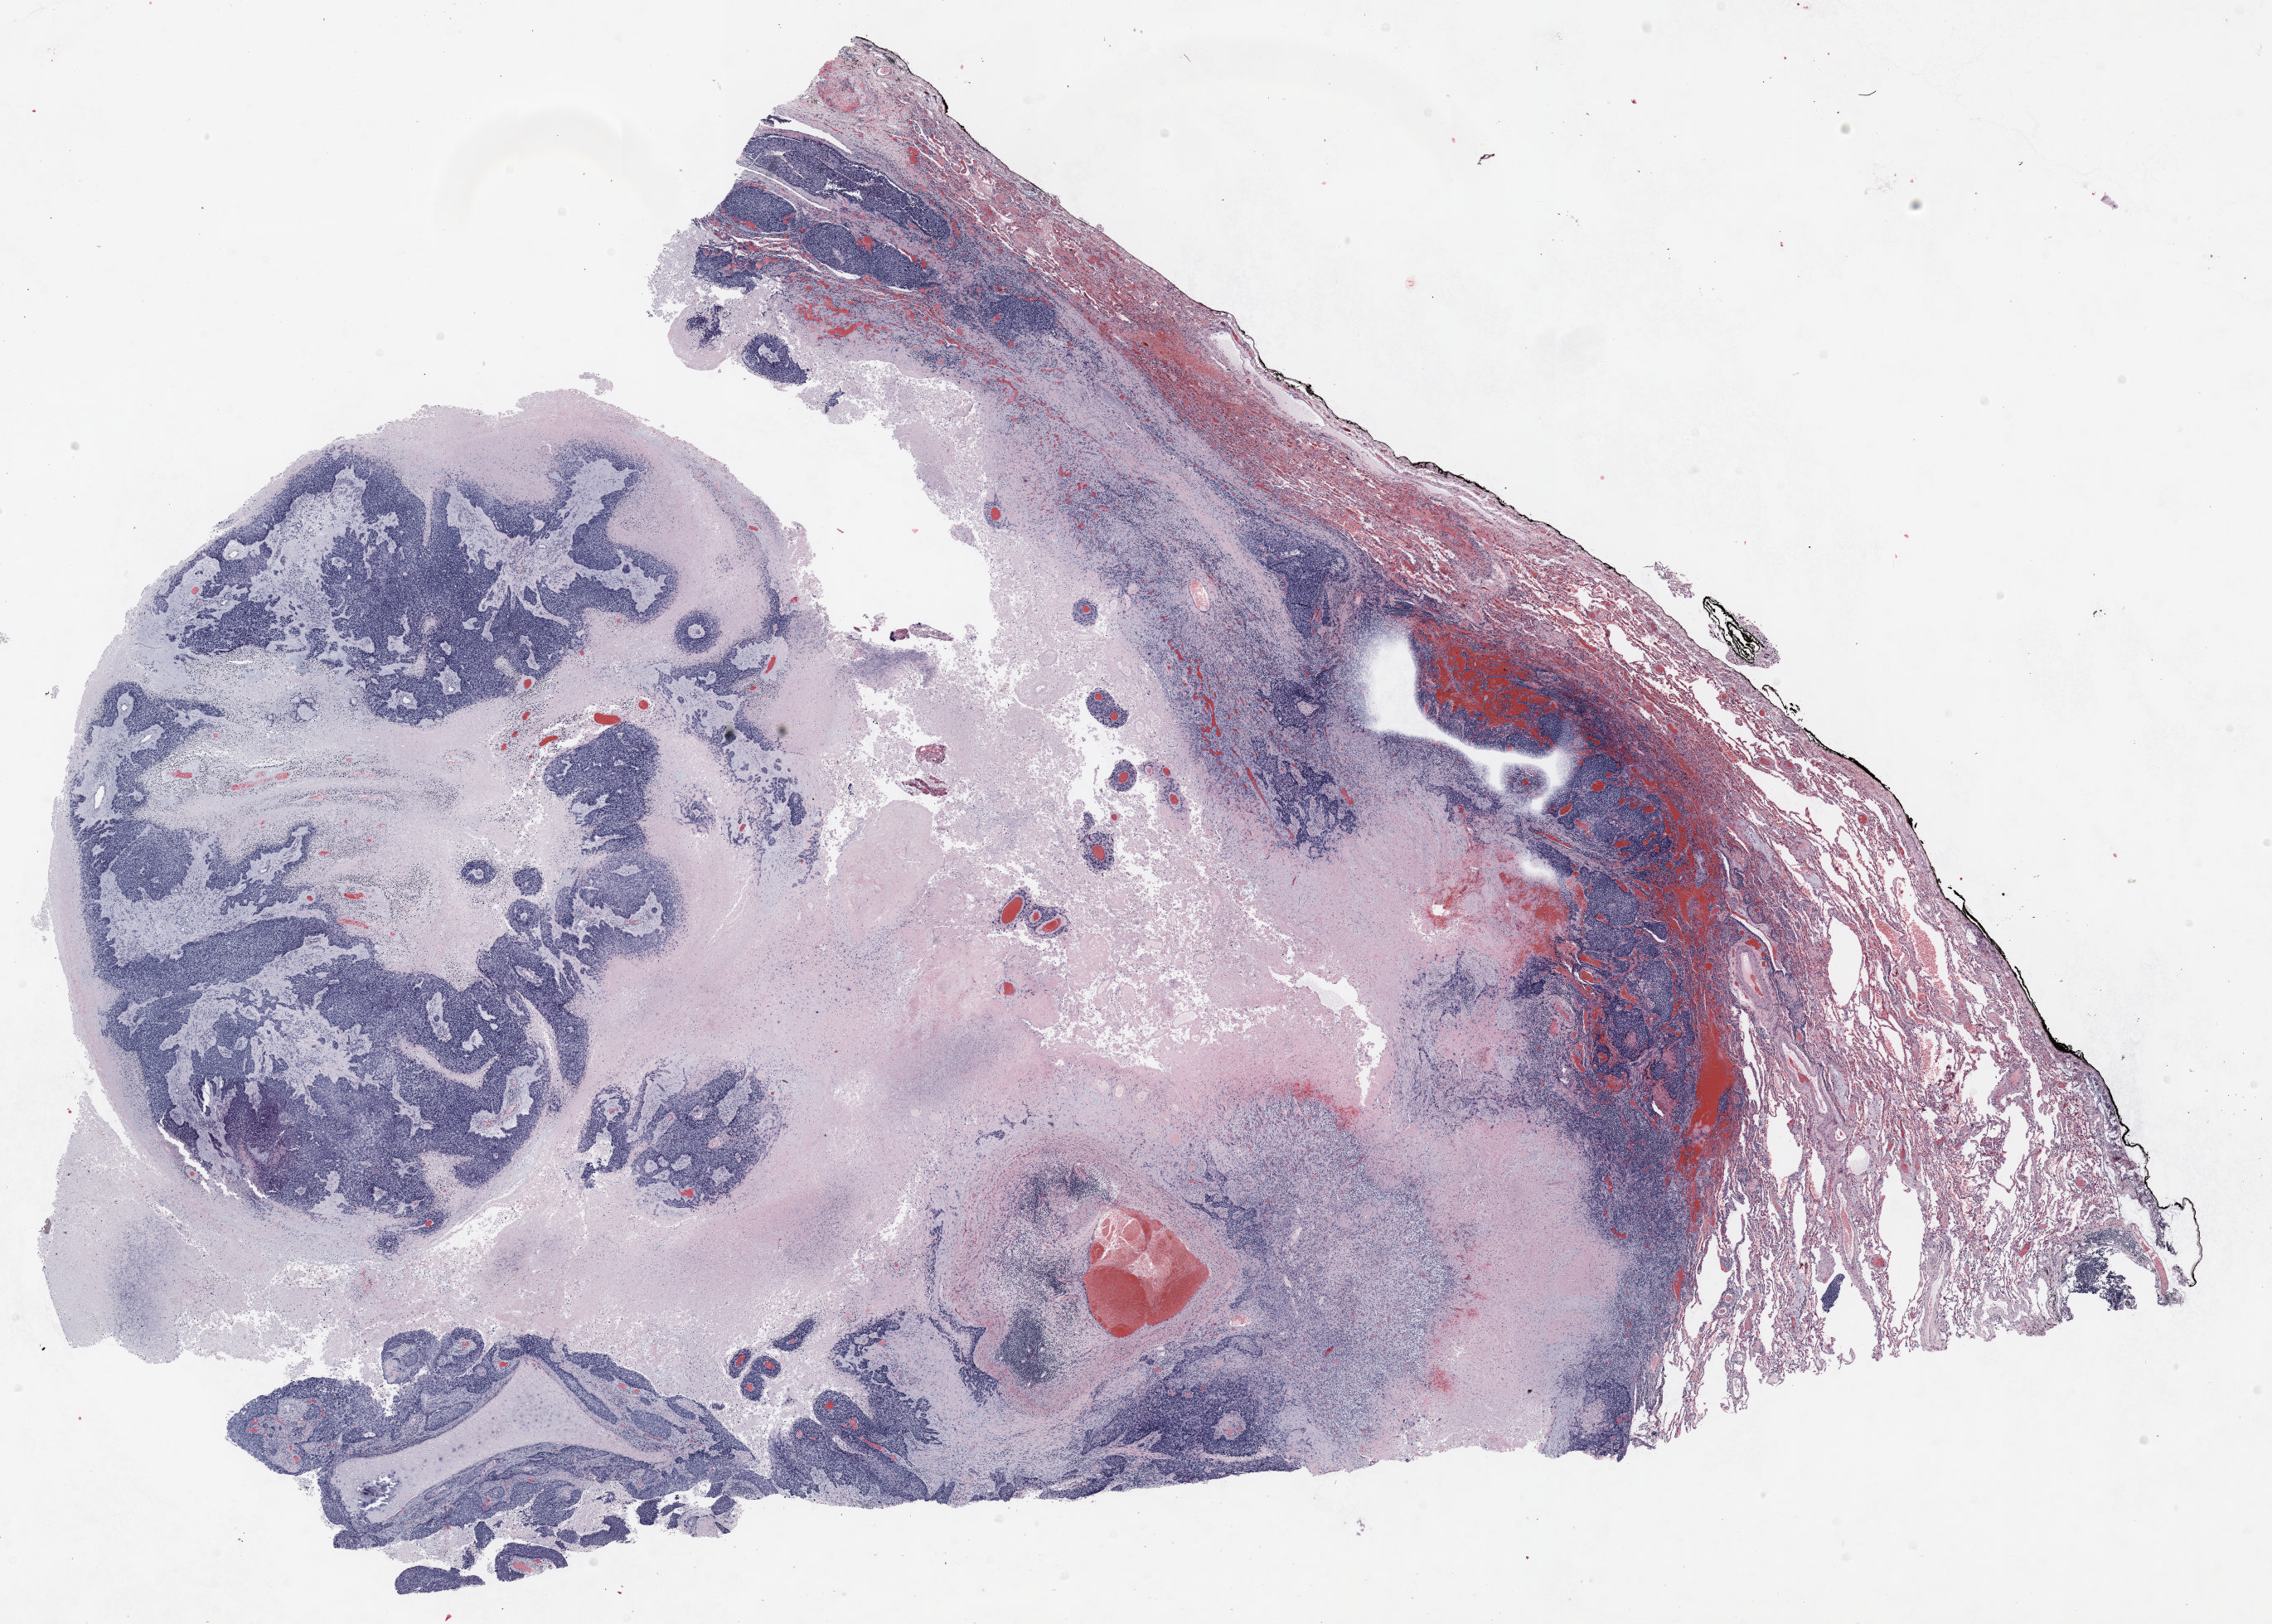
Hematoxylin and eosin (H&E) stained whole-slide image, shown as a low-resolution overview of the whole scanned area (about 22.0 x 15.7 mm). Formalin-fixed paraffin-embedded (FFPE) section. Lung tissue. Female, age 58 at enrolment. Grade: moderately differentiated (G2).
- participant's lung-cancer diagnosis: Squamous cell carcinoma, NOS
- tumour size (pathology): 17 mm
- primary tumour location (clinical record): right upper lobe
- stage (AJCC 6th edition): IA